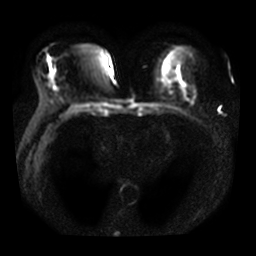
Breast MRI, one axial slice. Position 15 of 32 along the scan axis. Diffusion-weighted series; image 2 of 4 stored at this slice position (different b-values; order by instance number). 3 T. 5 mm slice thickness. 256 × 256 image matrix. Female patient.
Outlined on this slice (outlined manually by an expert reader):
- tumour on diffusion-weighted imaging: bounding box [x1, y1, x2, y2] px = [181, 86, 194, 103]